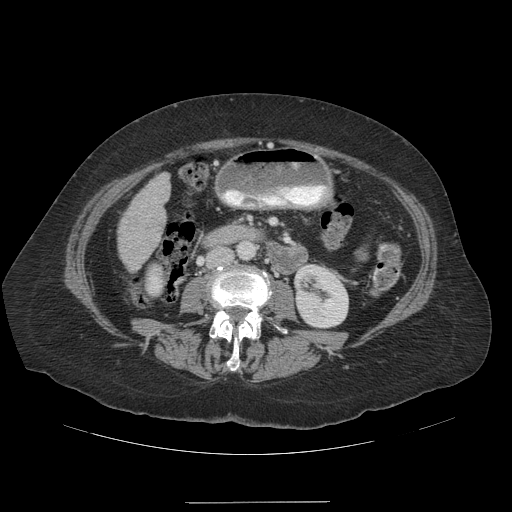
Contrast-enhanced abdominal CT (liver protocol), one axial slice. Position 34 of 99 along the scan axis. 140 kVp. Soft-tissue window (W 400 / L 40 HU). 2.5 mm slice thickness. 512 × 512 image matrix, field of view 440 × 440 mm. Case-level facts recorded for this patient, not image findings: diagnosis: hepatocellular carcinoma (patient treated with transarterial chemoembolisation; whether this scan precedes or follows treatment is not stated here); TNM stage (as recorded): Stage-IVA; Child-Pugh class: A; tumour nodularity: multinodular.
Structures marked on this image (semi-automatic segmentation, software-assisted and operator-edited):
- liver parenchyma outside the tumour (the mass and vessels are separate outlines, so this box may not span the whole liver): bounding box <118,173,170,270> (left, top, right, bottom; pixels)